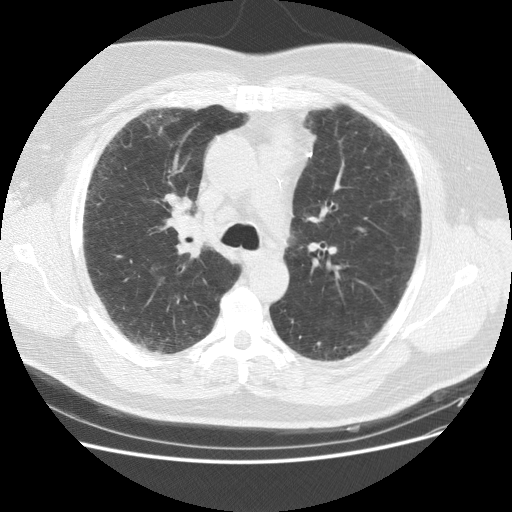
Low-dose screening chest CT, axial slice. Baseline annual screen. Lung window (W 1500 / L -600 HU). Standard (soft-tissue) reconstruction kernel (STANDARD). 120 kVp. 512 × 512 image matrix, field of view 378 × 378 mm. Male, age 59 years at enrolment. Current smoker at enrolment.
• Lesion marked by an expert reader, bounding box <163,203,204,242> (left, top, right, bottom; pixels).
• The screening reader recorded 2 non-calcified nodules or masses ≥4 mm on this exam; which of them this box marks is not recorded.
• Participant outcome: lung cancer diagnosed 338 days after this screen — adenocarcinoma, NOS, right upper lobe, right middle lobe, moderately differentiated (G2), stage IA (AJCC 6th edition), 13 mm at pathology.